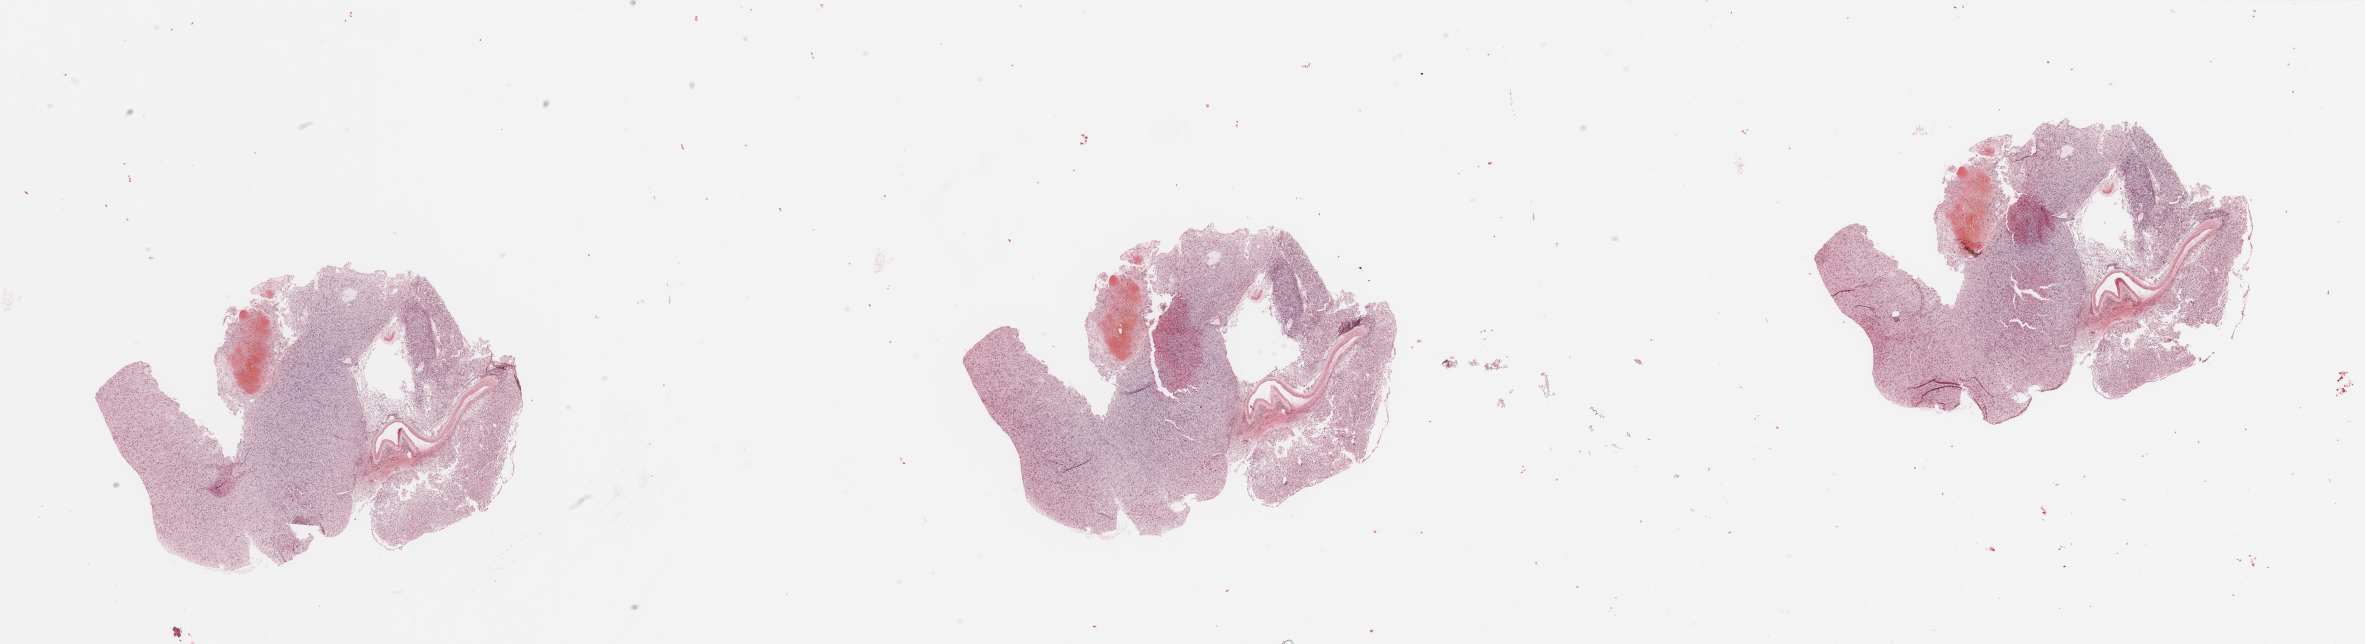
Hematoxylin and eosin (H&E) stained whole-slide image — shown as a low-resolution overview of the whole scanned area (about 37.4 x 10.2 mm, from a 20x scan), brain, tumour tissue. Male, 70 y/o.
• primary tumour site (as recorded): frontal lobe
• histologic diagnosis: Glioblastoma